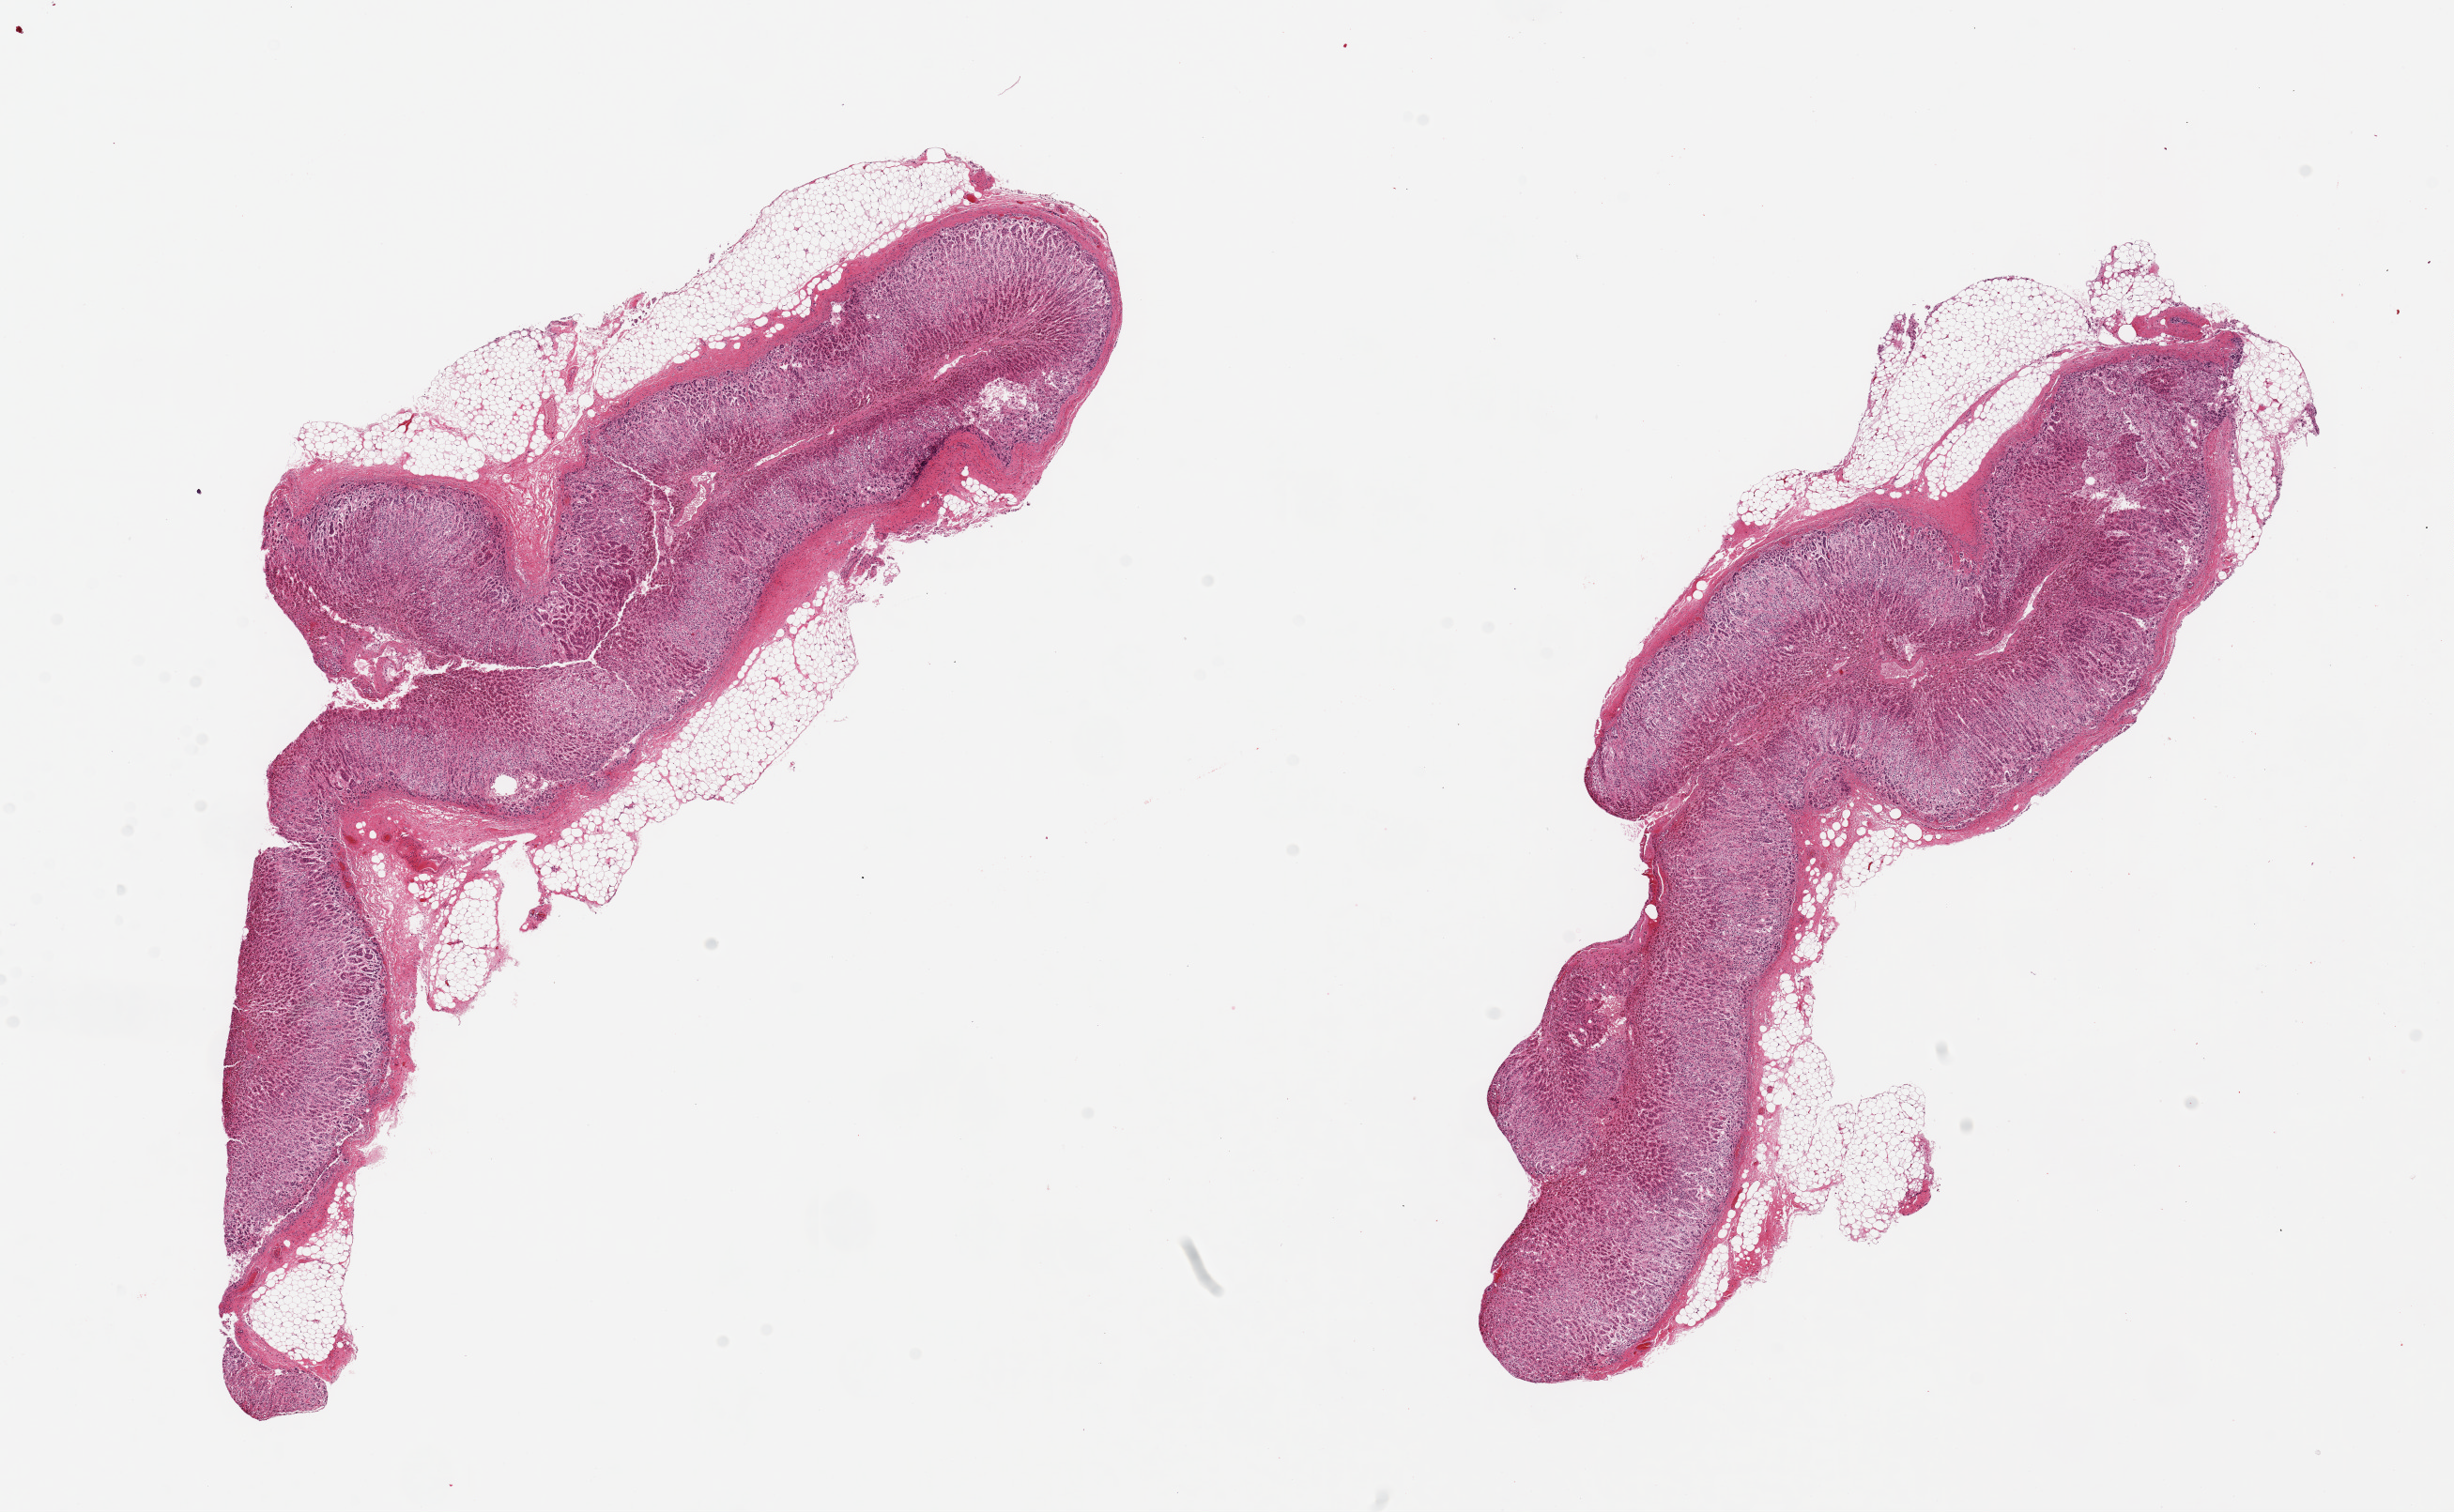
Digitized haematoxylin and eosin-stained section, low-resolution overview of the scanned area, about 20.7 x 12.7 mm (from a 20x scan); PAXgene-fixed paraffin-embedded (PFPE) section; sampled site (target tissue): adrenal gland; tissue donor sample. Donor: male.
- review note (as recorded): 2 pieces, 12x5 & 11x4mm; ~80% cortex, 20% adherent fat